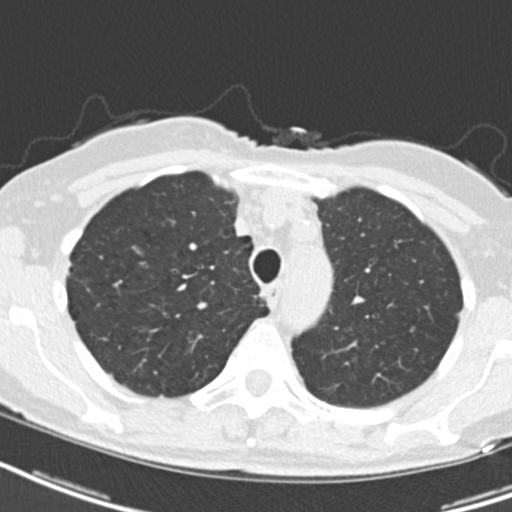
Axial slice from a low-dose chest CT screening exam; baseline annual screen; lung window (W 1500 / L -600 HU); standard (soft-tissue) reconstruction kernel (B30f). Female participant, aged 68 years at enrolment. Current smoker at enrolment.
Expert-annotated lung lesion, bounding box [x1, y1, x2, y2] px = [247, 285, 271, 314]. No non-calcified nodule or mass ≥4 mm was recorded by the screening reader at this exam. Participant outcome: lung cancer diagnosed 807 days after this screen (after the third annual screen) — squamous cell carcinoma, NOS, right upper lobe, mediastinum, poorly differentiated (G3), stage IIIB (AJCC 6th edition), 43 mm at pathology.